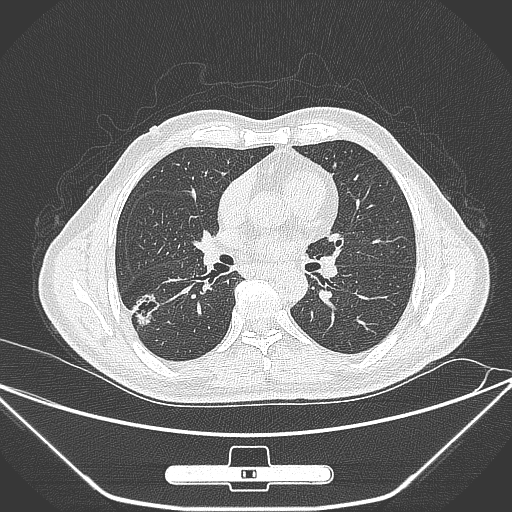
Chest CT, one axial slice; position 148 of 309 along the scan axis; lung window (W 1500 / L -600 HU); 1 mm slice thickness; 512 × 512 image matrix, field of view 398 × 398 mm. Patient: male, 71 years. Case-level facts recorded for this patient, not image findings: clinical TNM (as recorded): T1c N0 M0; histopathological grade: G2.
Structures marked on this image (rectangle marked by the reading radiologist):
- lung tumour (recorded histology: adenocarcinoma): bounding box (x1, y1, x2, y2) in pixels: (129, 290, 165, 328)